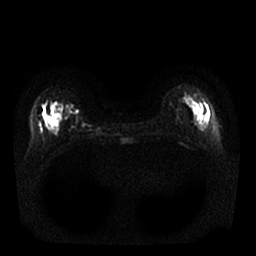
Breast MRI, one axial slice. Position 7 of 25 along the scan axis. Diffusion-weighted series; image 2 of 4 stored at this slice position (different b-values; order by instance number). 1.5 T. 256 × 256 image matrix, field of view 340 × 340 mm. Female patient.
Annotated regions visible in this slice (outlined manually by an expert reader):
- tumour on diffusion-weighted imaging: bounding box <46,124,48,128> (left, top, right, bottom; pixels)